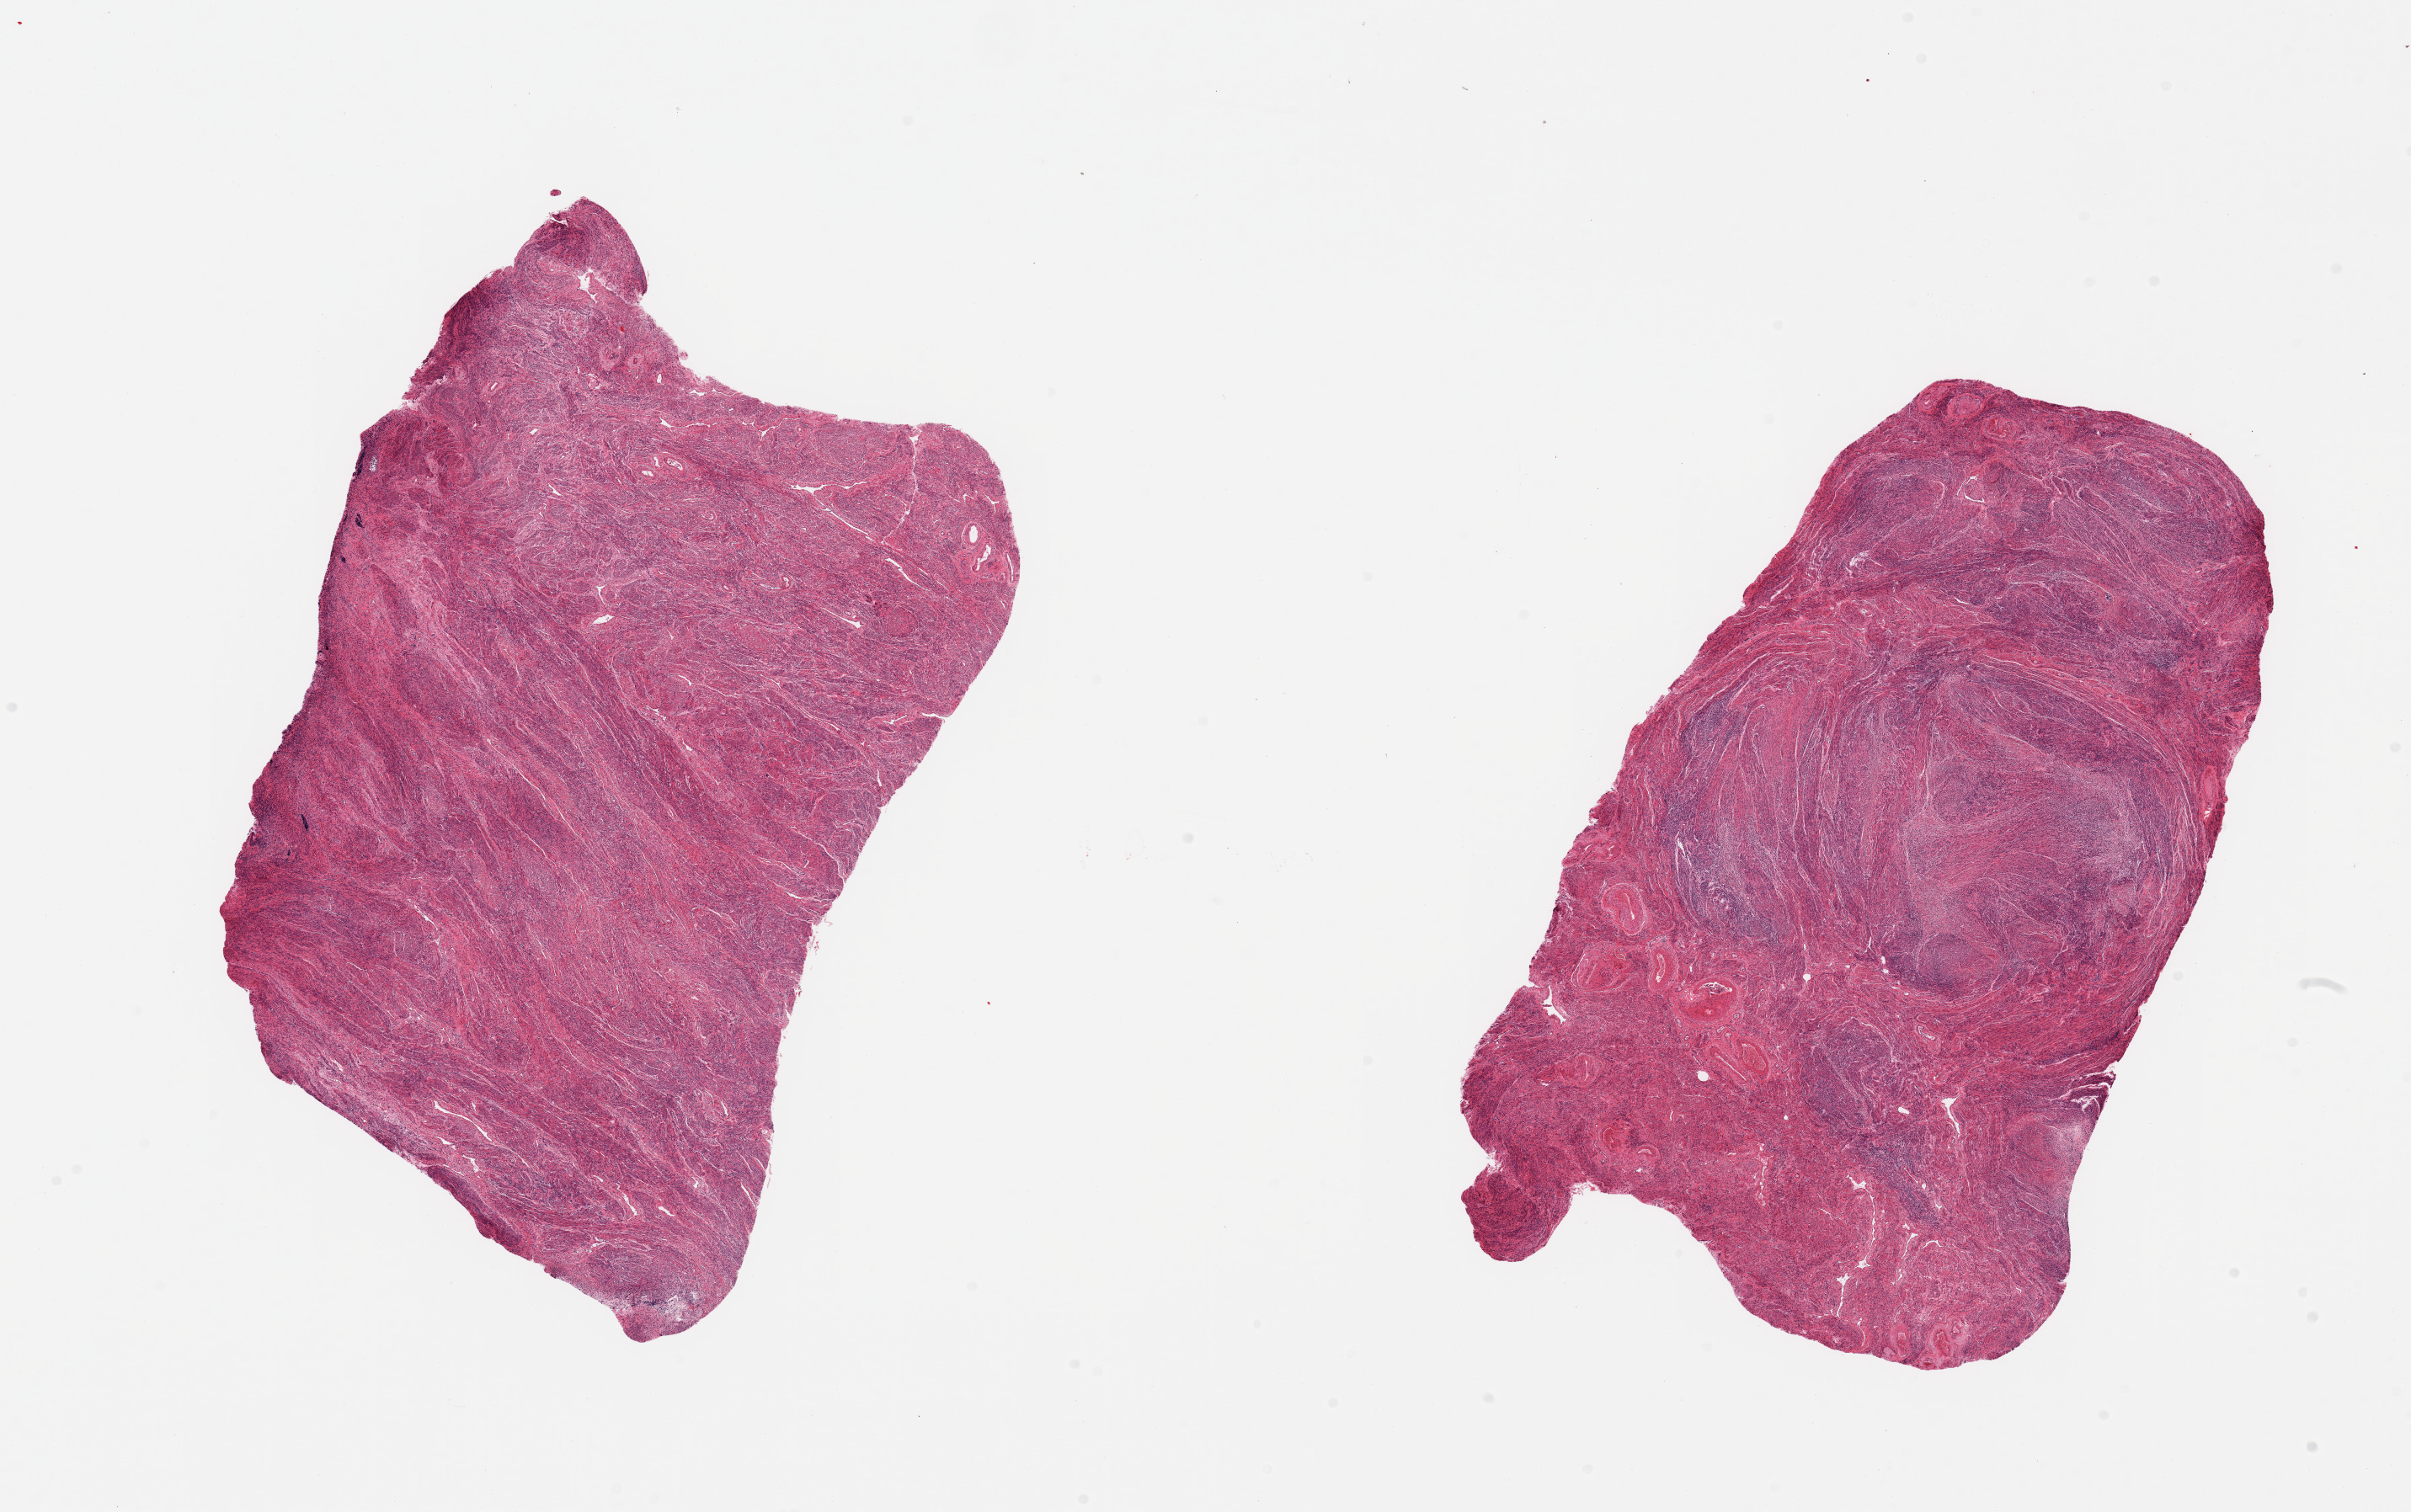
Digitized haematoxylin and eosin-stained section, brightfield, whole scanned area (about 22.6 x 14.2 mm, slide scanned at 20x) shown as a low-resolution overview; PAXgene-fixed, paraffin-embedded tissue; target tissue: uterus; donor tissue sample. Donor sex: female.
Reviewer comment on this tissue sample: 2 pieces; myometrium only; no endometrium.